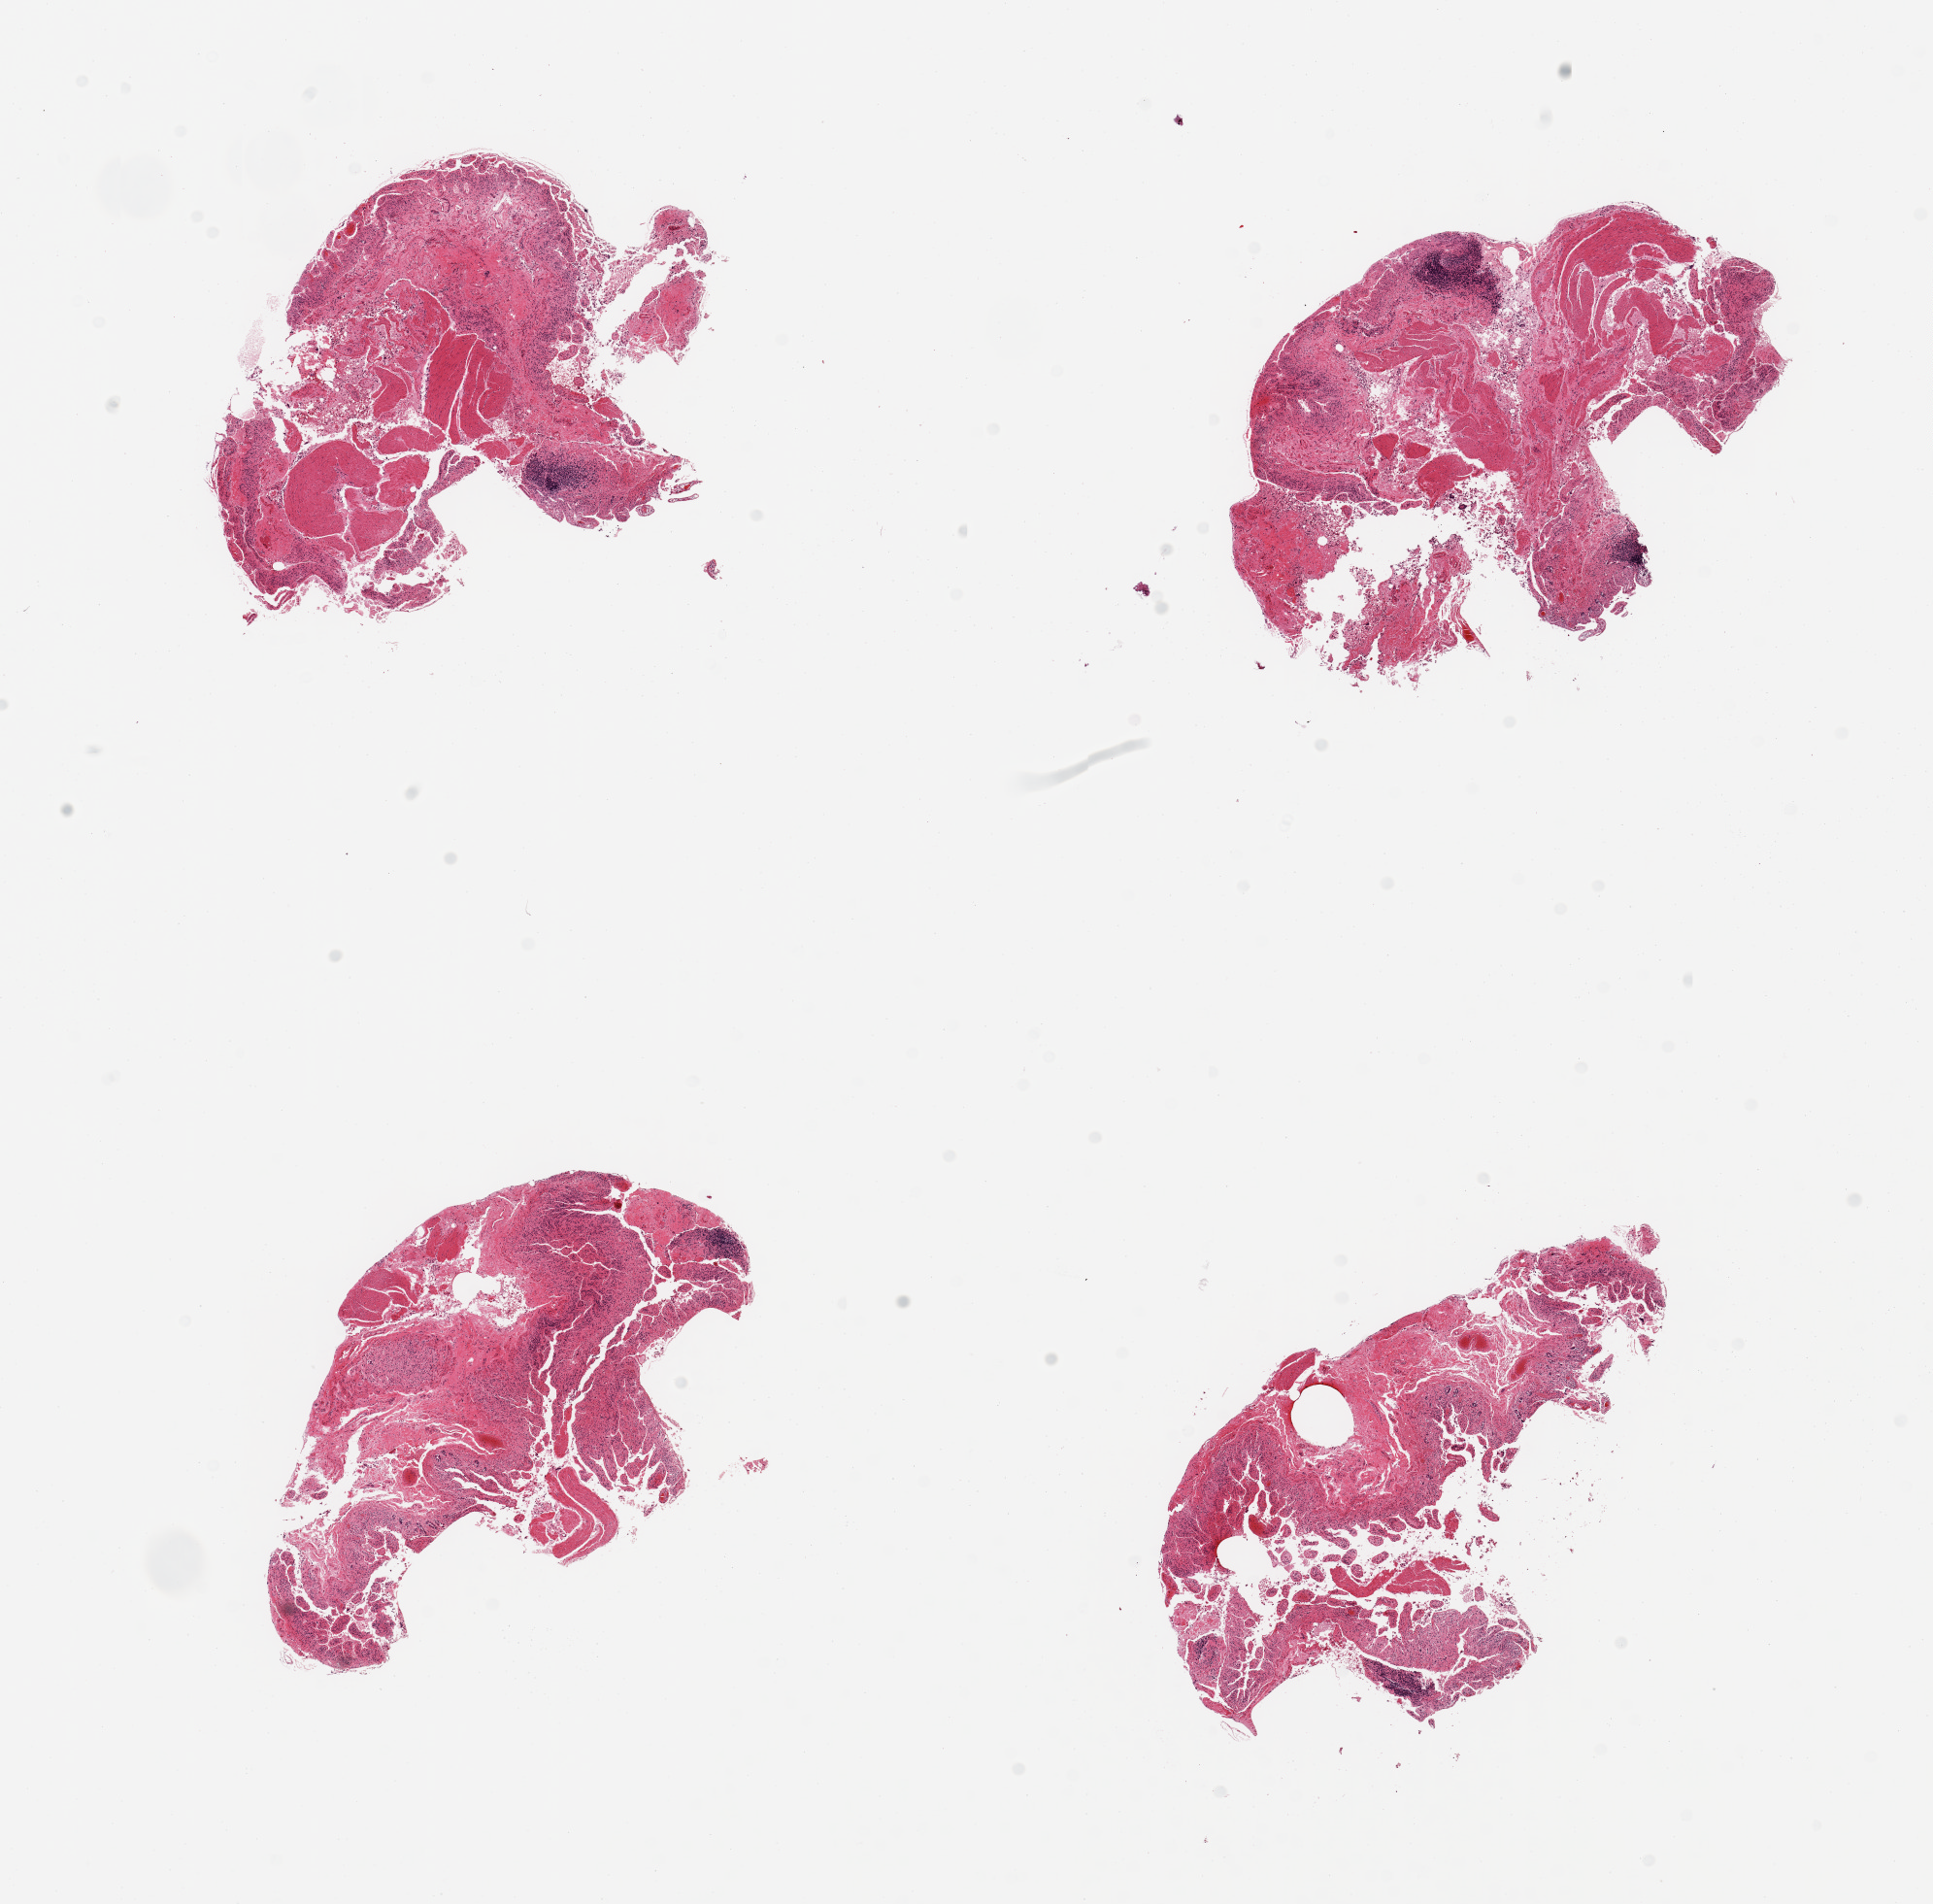
Digitized H&E-stained section, brightfield, whole scanned area (about 15.8 x 15.5 mm) shown as a low-resolution overview. Donor: male.
Specimen: PAXgene-fixed, paraffin-embedded tissue; sampled site (target tissue): ileum; tissue donor sample.